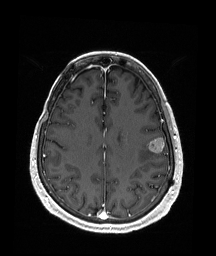
Brain MRI from a brain-tumour surgery series, one axial slice; T1-weighted post-contrast; 1 mm slice thickness; 216 × 256 image matrix, field of view 211 × 250 mm. Case-level facts recorded for this patient, not image findings: histopathology: Metastatic Malignant Melanoma; tumour location: Left Frontal.
Annotated regions visible in this slice (expert manual segmentation):
- tumour: bounding box [x1, y1, x2, y2] px = [148, 138, 165, 153]